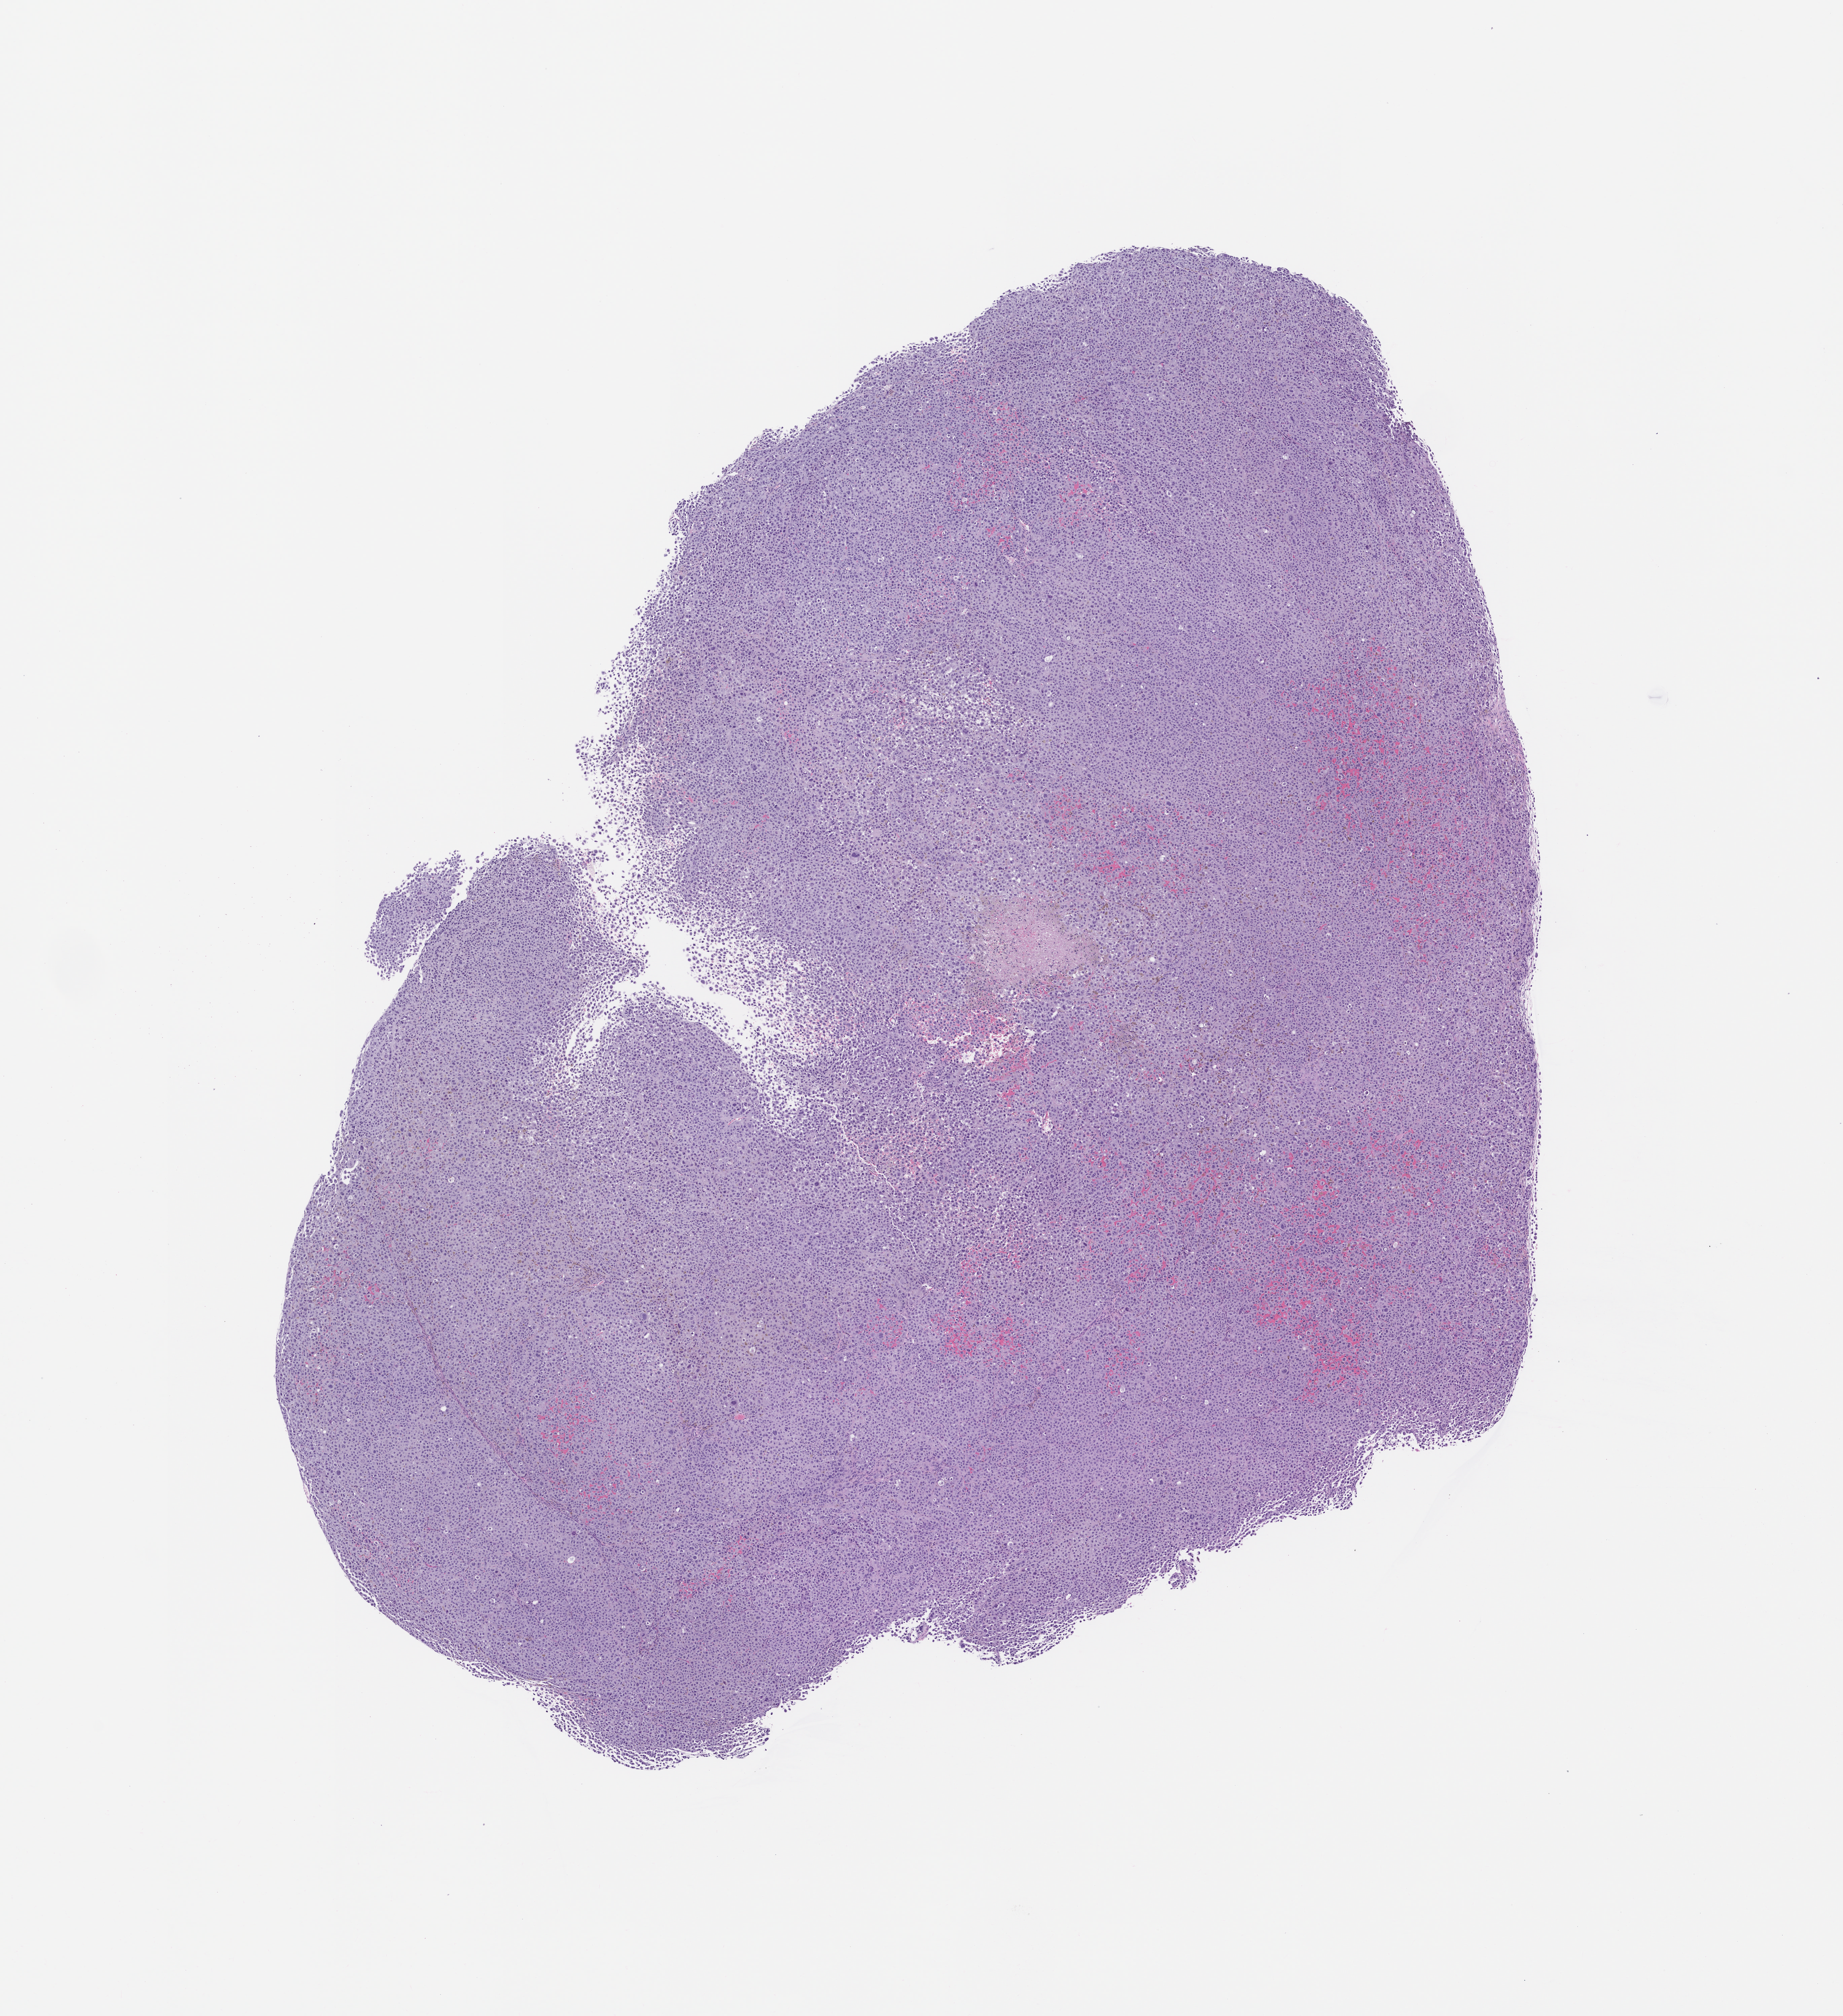
H&E whole-slide image of a patient-derived xenograft (PDX) tumor grown in a mouse, passage 2, whole scanned area (about 11.0 x 12.0 mm) shown as a low-resolution overview. Formalin-fixed paraffin-embedded section. Tumor site category: skin.
Originating patient diagnosis: Melanoma.